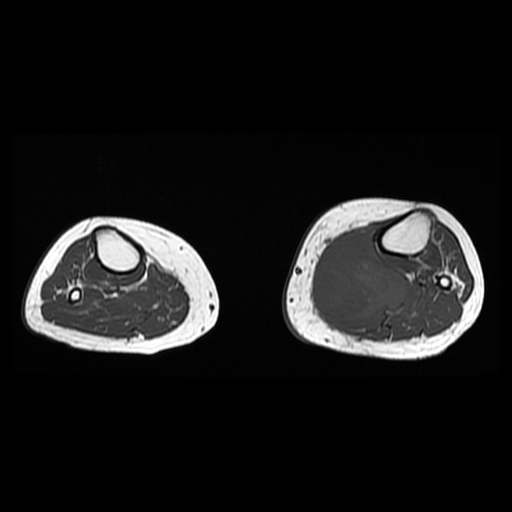
MRI of an extremity soft-tissue mass, one axial slice; 6 mm slice thickness; 512 × 512 image matrix, field of view 330 × 330 mm. Female patient. Case-level facts recorded for this patient, not image findings: histological type: extraskeletal high grade osteogenic sarcoma; grade: high; site of the primary tumour: left calf.
Structures marked on this image (outlined manually by an expert reader):
- gross tumour volume (mass): box from (x=312, y=230) to (x=409, y=323) px